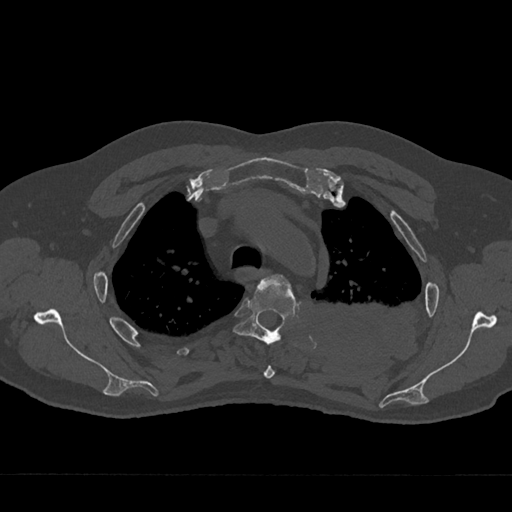
CT including the spine, one axial slice. Position 532 of 797 along the scan axis. Reconstruction kernel Br40s/3. Bone window (W 1800 / L 400 HU). 0.5 mm slice thickness. 512 × 512 image matrix, field of view 377 × 377 mm. Male patient, age 75 years. Case-level facts recorded for this patient, not image findings: primary cancer: renal; vertebrae with lytic lesions (as recorded): T4.
Annotated regions visible in this slice (semi-automatically segmented with operator editing):
- T3 vertebra: box from (x=263, y=275) to (x=289, y=379) px
- T4 vertebra: (x=232, y=276)–(x=296, y=345)